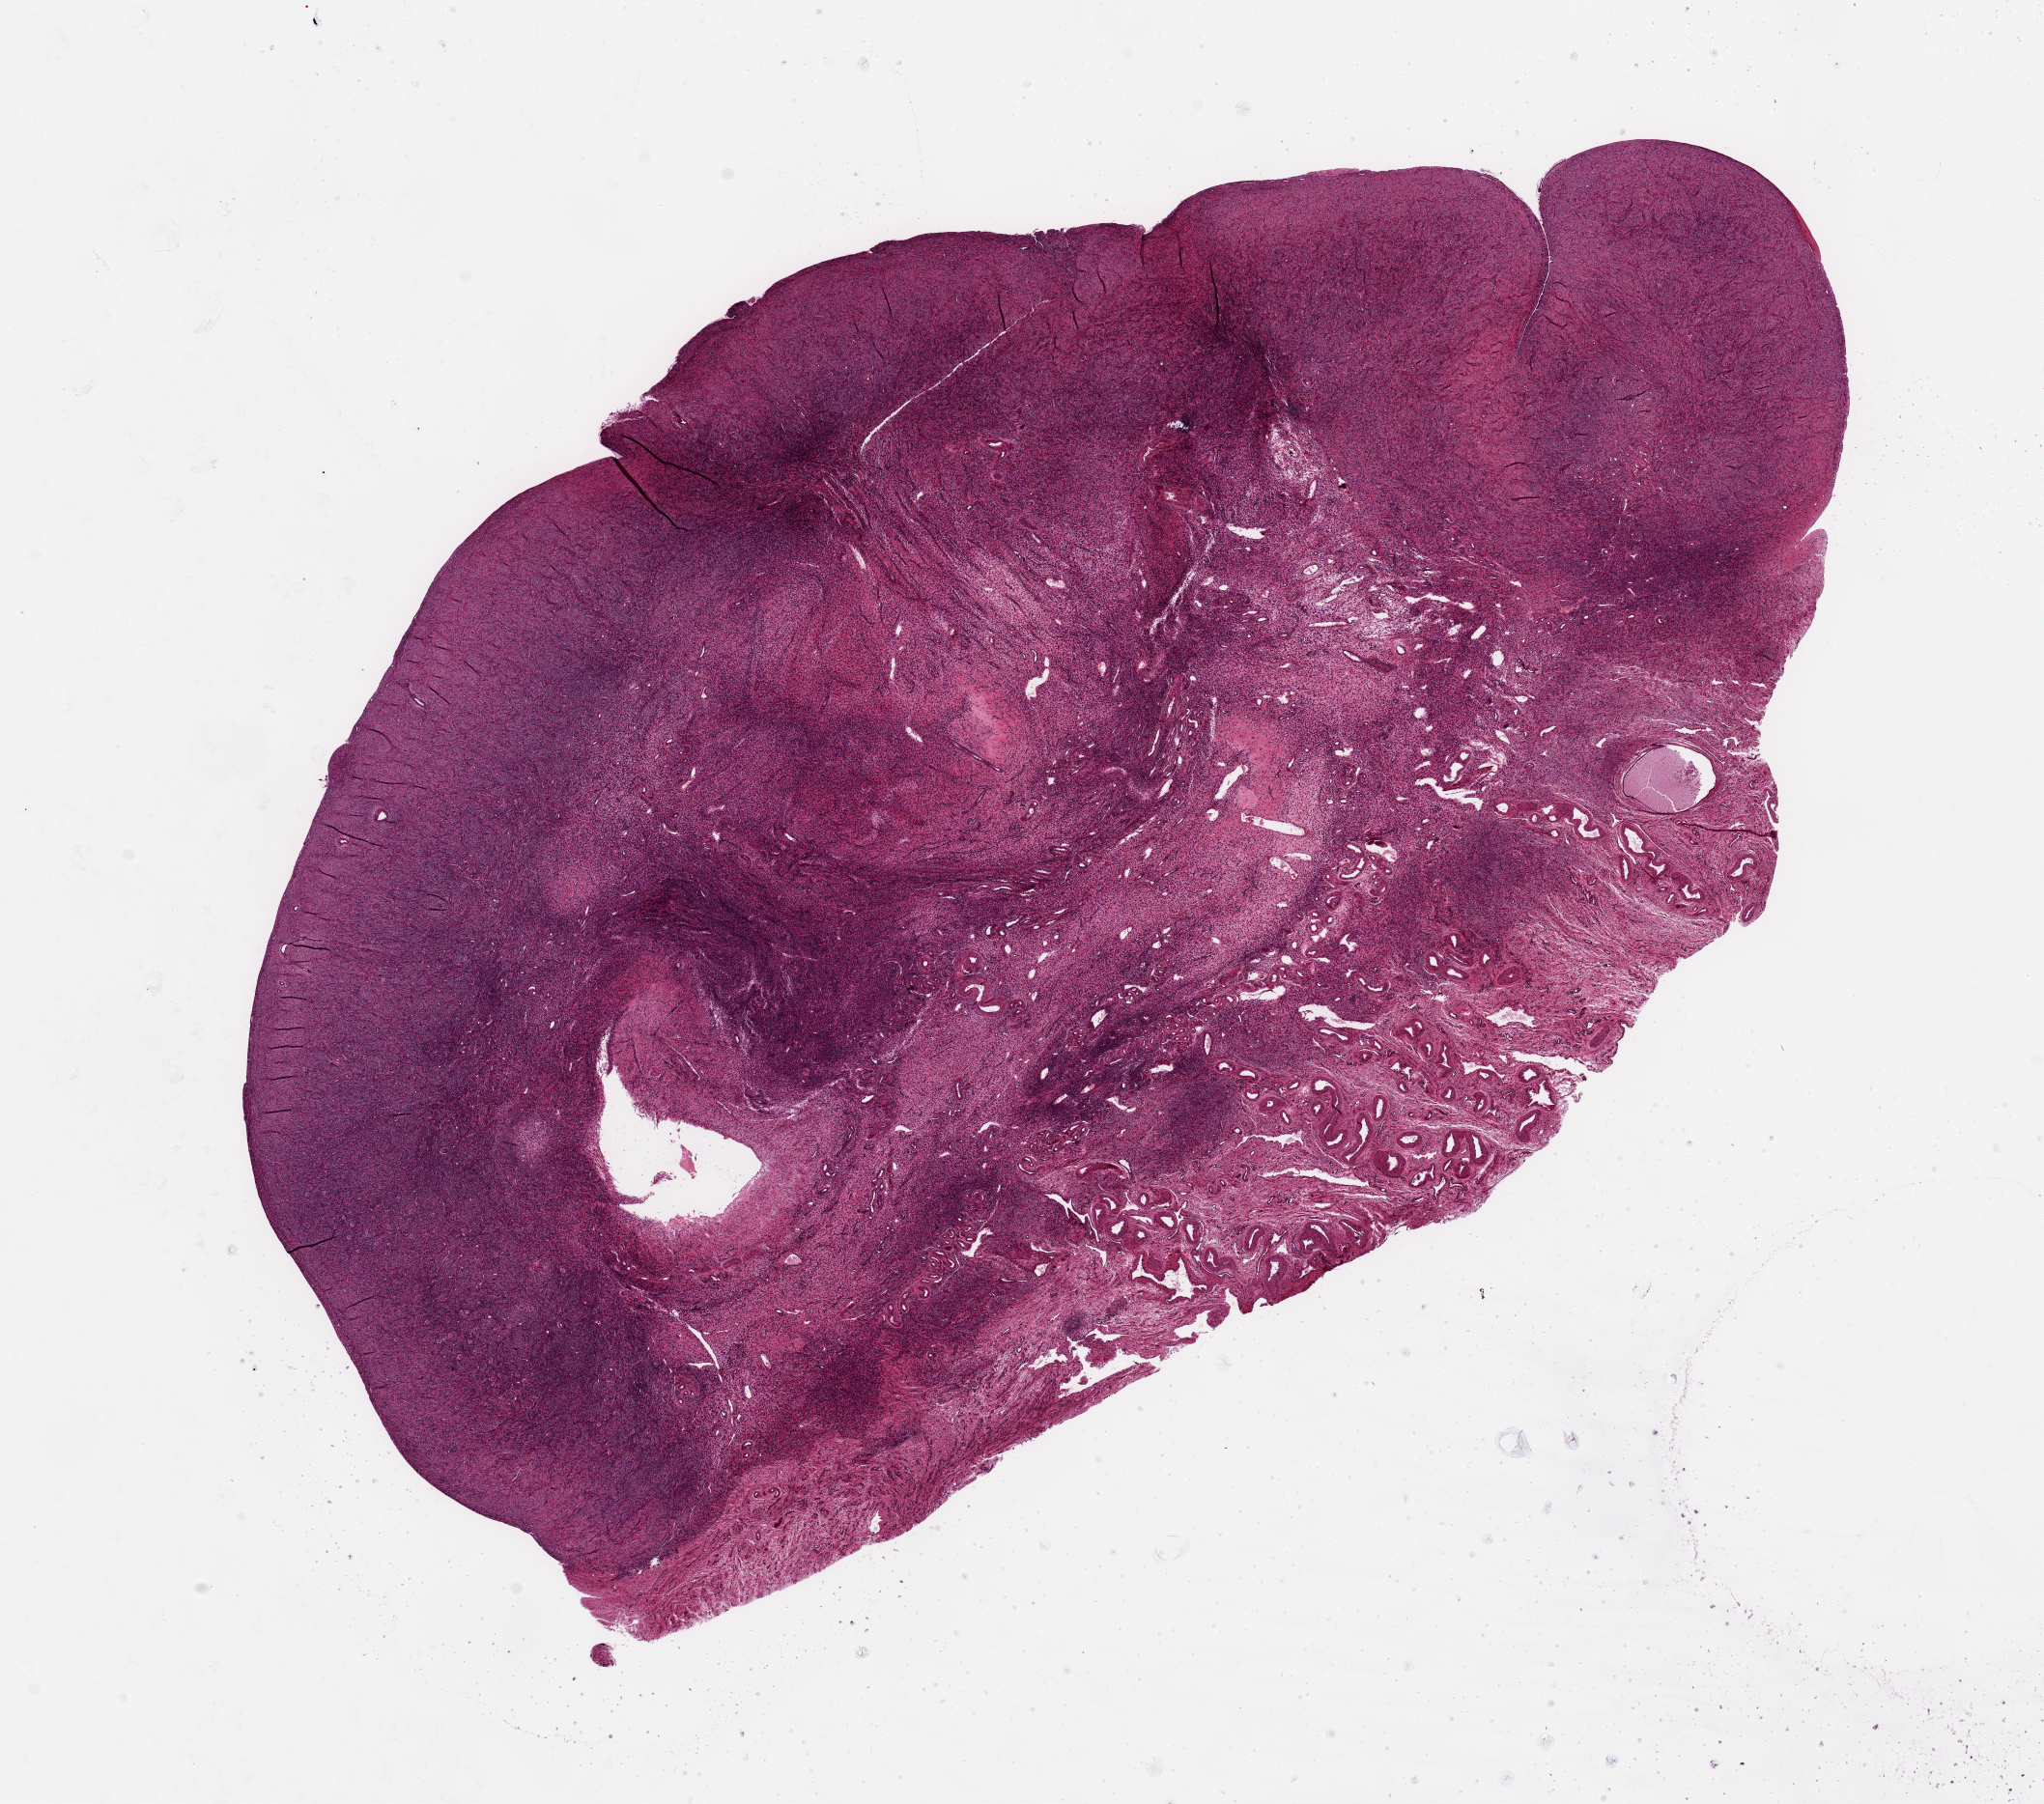
Whole-slide image, haematoxylin and eosin stain, brightfield, low-resolution overview of the scanned area, about 16.7 x 14.8 mm (acquisition: 20x scan). PAXgene-fixed paraffin-embedded (PFPE) section. Sampled site (target tissue): ovary. Donor tissue sample. Donor: female.
• reviewer comment on this tissue sample: 15x9mm, postmenopausal